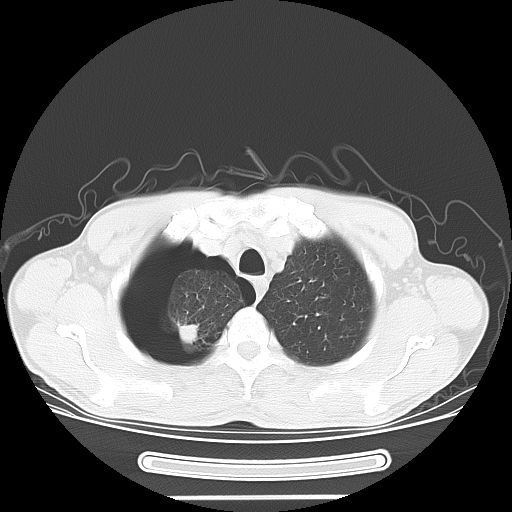
Chest CT, one axial slice; slice 57 of 67 in the series (ordered by position); reconstruction kernel LUNG; 120 kVp; lung window (W 1500 / L -600 HU); 512 × 512 image matrix. Male patient. Case-level facts recorded for this patient, not image findings: clinical TNM (as recorded): T1c N0 M0.
Annotated regions visible in this slice (bounding box drawn by a radiologist):
- lung tumour (recorded histology: adenocarcinoma): bounding box <173,318,204,353> (left, top, right, bottom; pixels)